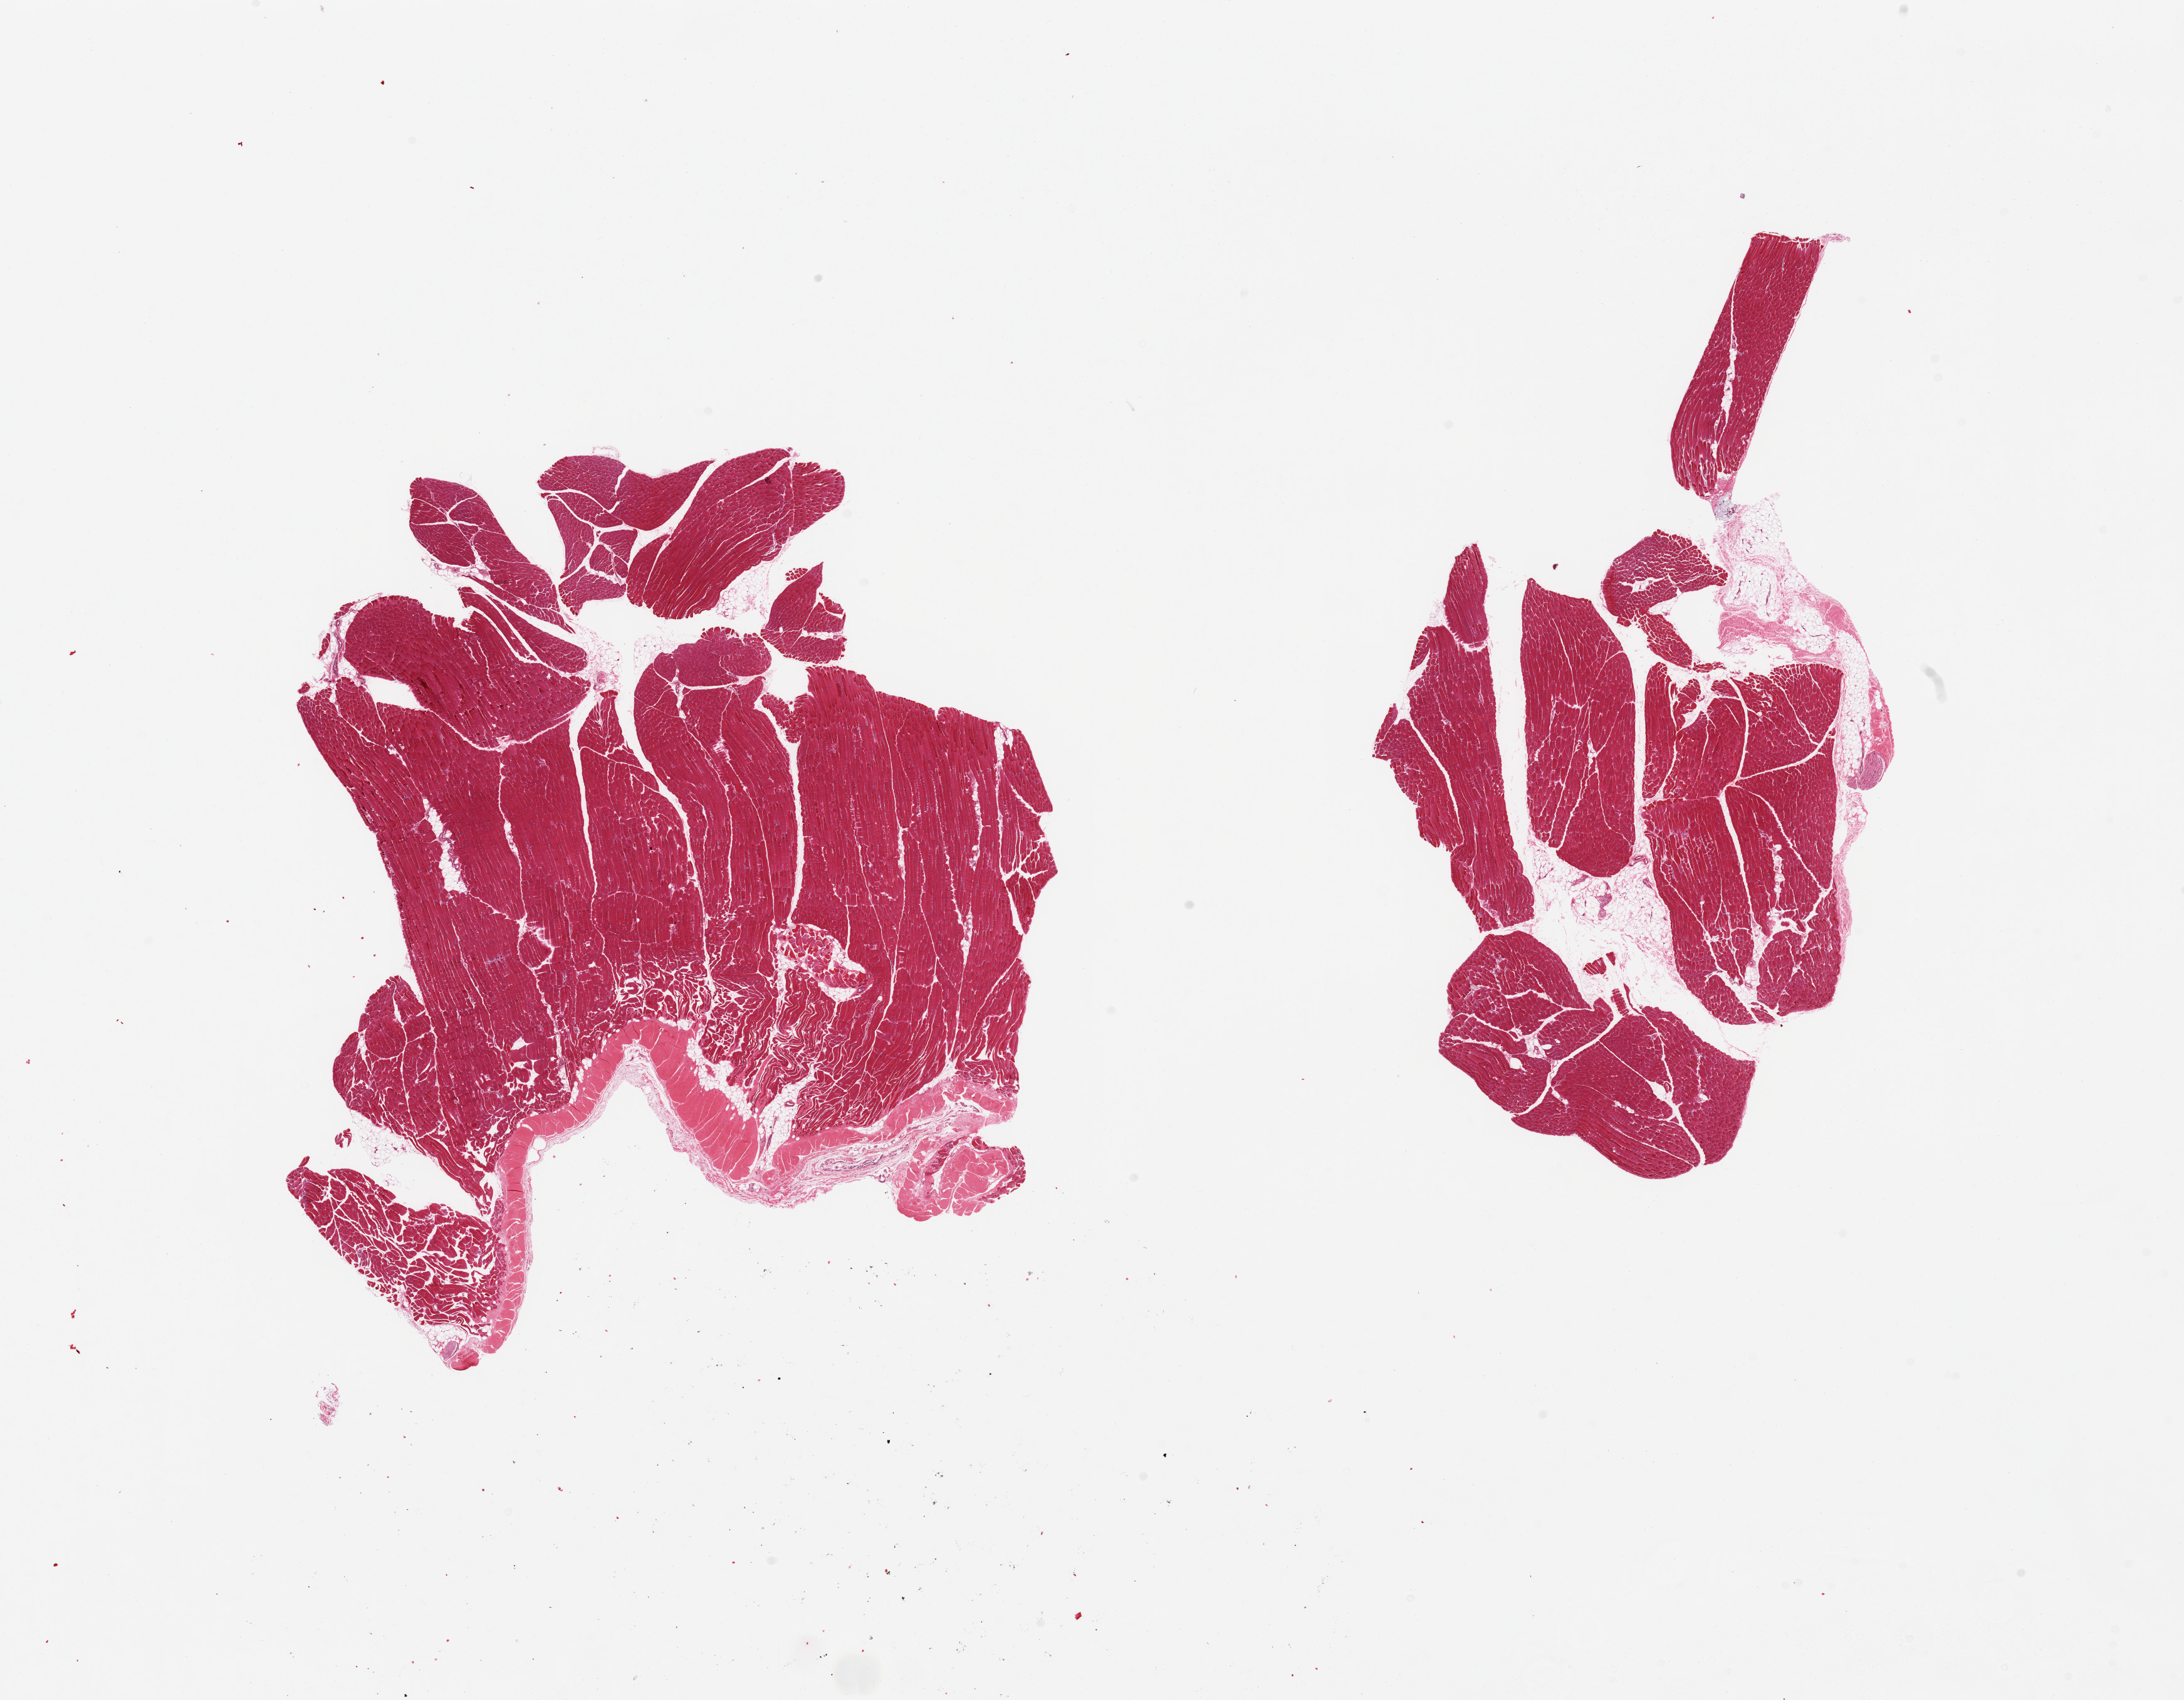
Whole-slide image, haematoxylin and eosin stain, shown as a low-resolution overview of the whole scanned area (about 27.6 x 21.5 mm); PAXgene-fixed, paraffin-embedded tissue; target tissue: skeletal muscle; donor tissue sample. Donor sex: female.
Pathologist's review note for this sample: 2 pieces.